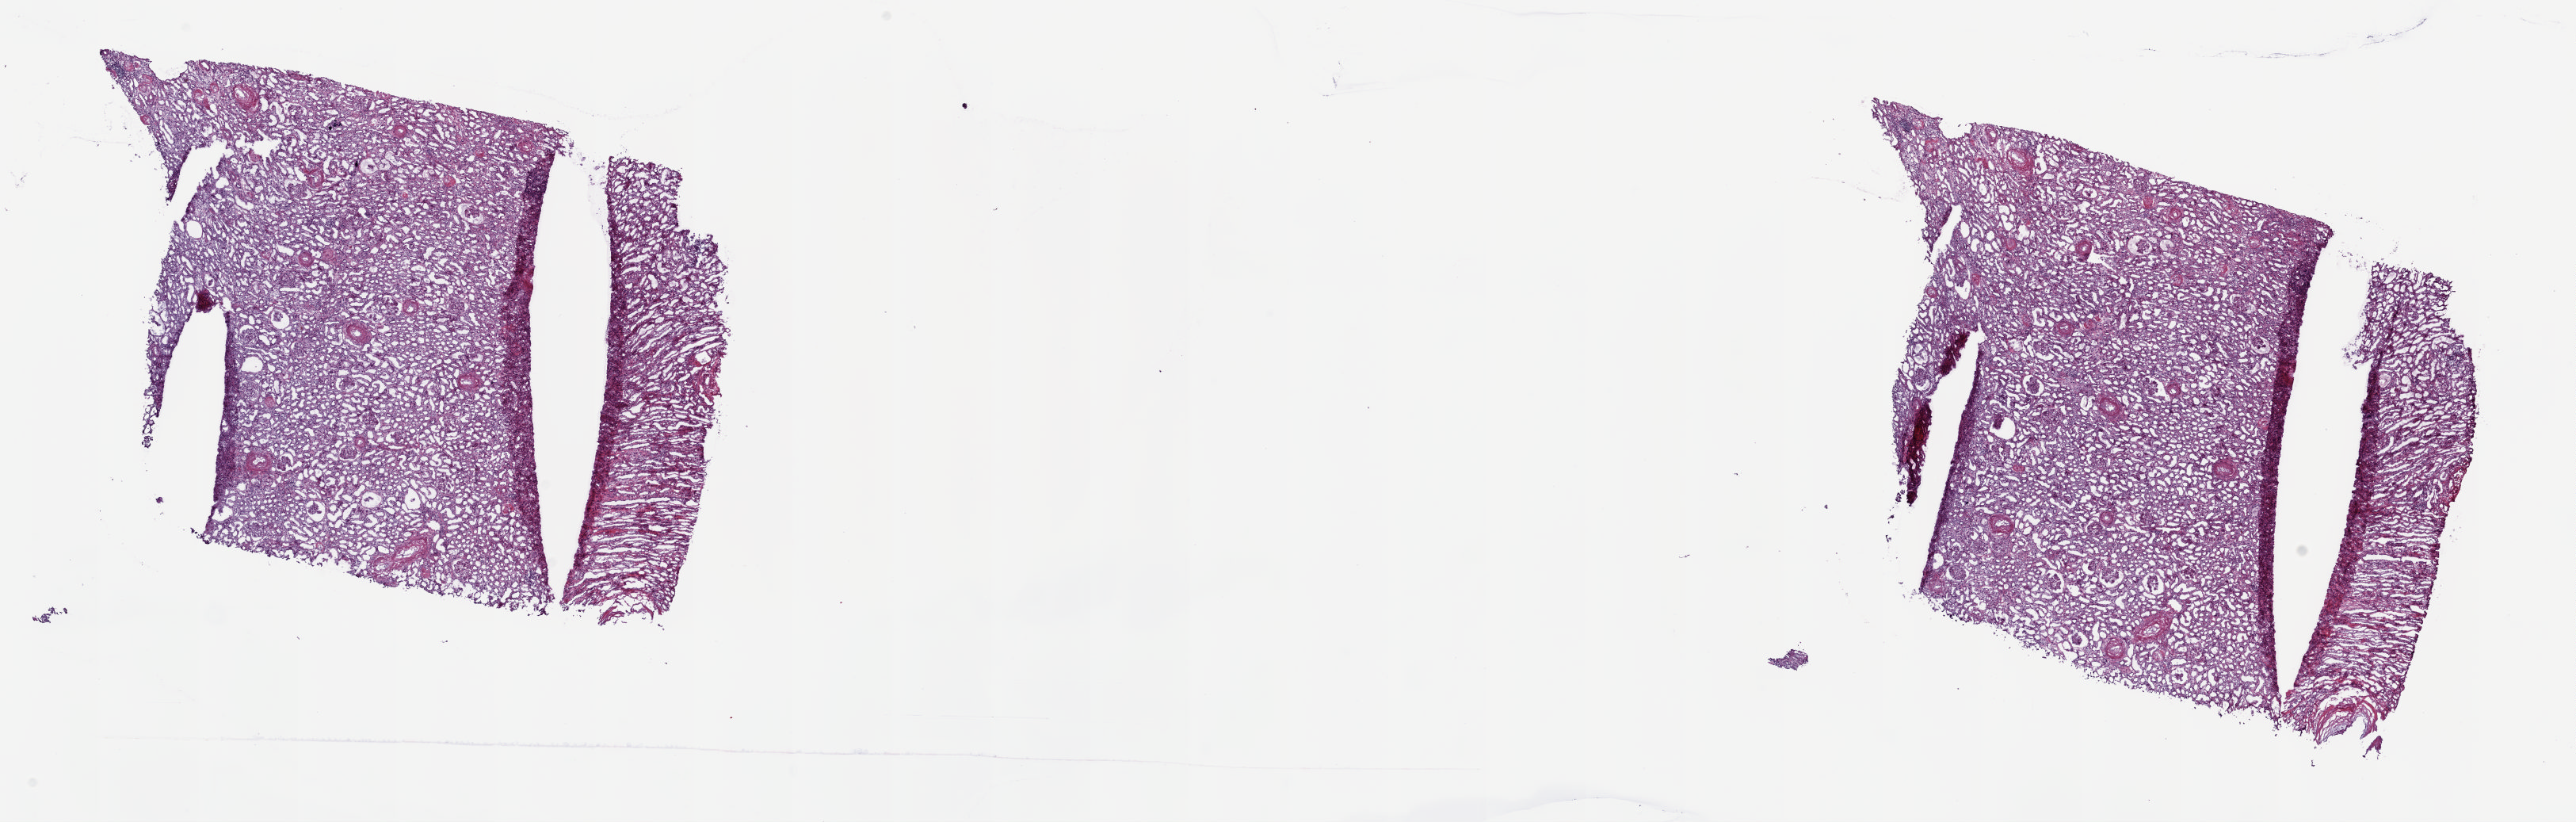
Whole-slide histology image, H&E — a low-resolution overview of the entire scanned area, about 25.8 x 8.2 mm (slide scanned at 20x). Frozen section from the top of the tissue portion. Sample: solid tissue normal (non-tumour tissue), colon. Patient: male, age at initial diagnosis 65 years. Pathologist review of this section (percent, as recorded): tumour cells 0%, tumour nuclei 0%.
This section: solid tissue normal sample (biorepository sample class). Patient diagnosis: Dedifferentiated liposarcoma (descending colon).